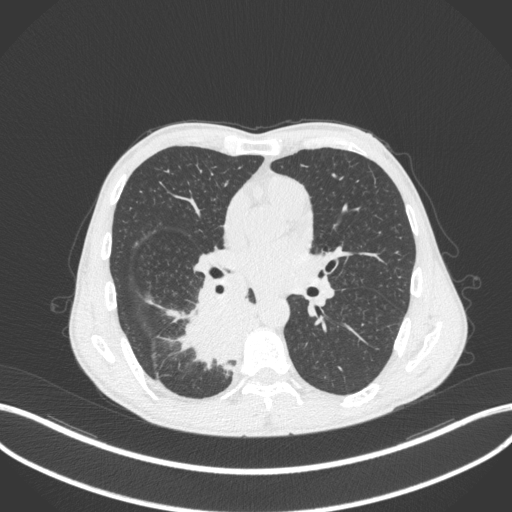
Chest CT, one axial slice. Position 194 of 371 along the scan axis. 120 kVp. Lung window (W 1500 / L -600 HU). 512 × 512 image matrix. Male patient, age 58 years. Case-level facts recorded for this patient, not image findings: clinical TNM (as recorded): T3 N1 M1.
Annotated regions visible in this slice (bounding box drawn by a radiologist):
- lung tumour (recorded histology: squamous cell carcinoma): bounding box (x1, y1, x2, y2) in pixels: (169, 288, 250, 366)